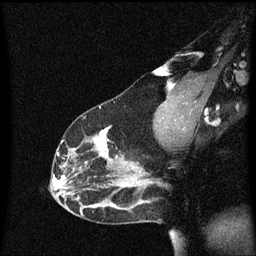
Breast MRI (dynamic contrast-enhanced), one sagittal slice; position 38 of 60 along the scan axis; dynamic contrast-enhanced series, image 2 of 3 at this slice position (ordered by acquisition); 1.5 T; TE 4.2 ms, TR 8.4 ms; 2 mm slice thickness; 256 × 256 image matrix, field of view 200 × 200 mm. Female patient, age 33 years.
Outlined on this slice (semi-automatic segmentation, software-assisted and operator-edited):
- analysis volume of interest (the breast-tissue region the enhancement analysis was run in; not a lesion): bounding box <51,116,152,191> (left, top, right, bottom; pixels)
- tumour enhancement mask (voxels above the 70 % enhancement threshold inside the analysis volume of interest): <55,126,119,185>